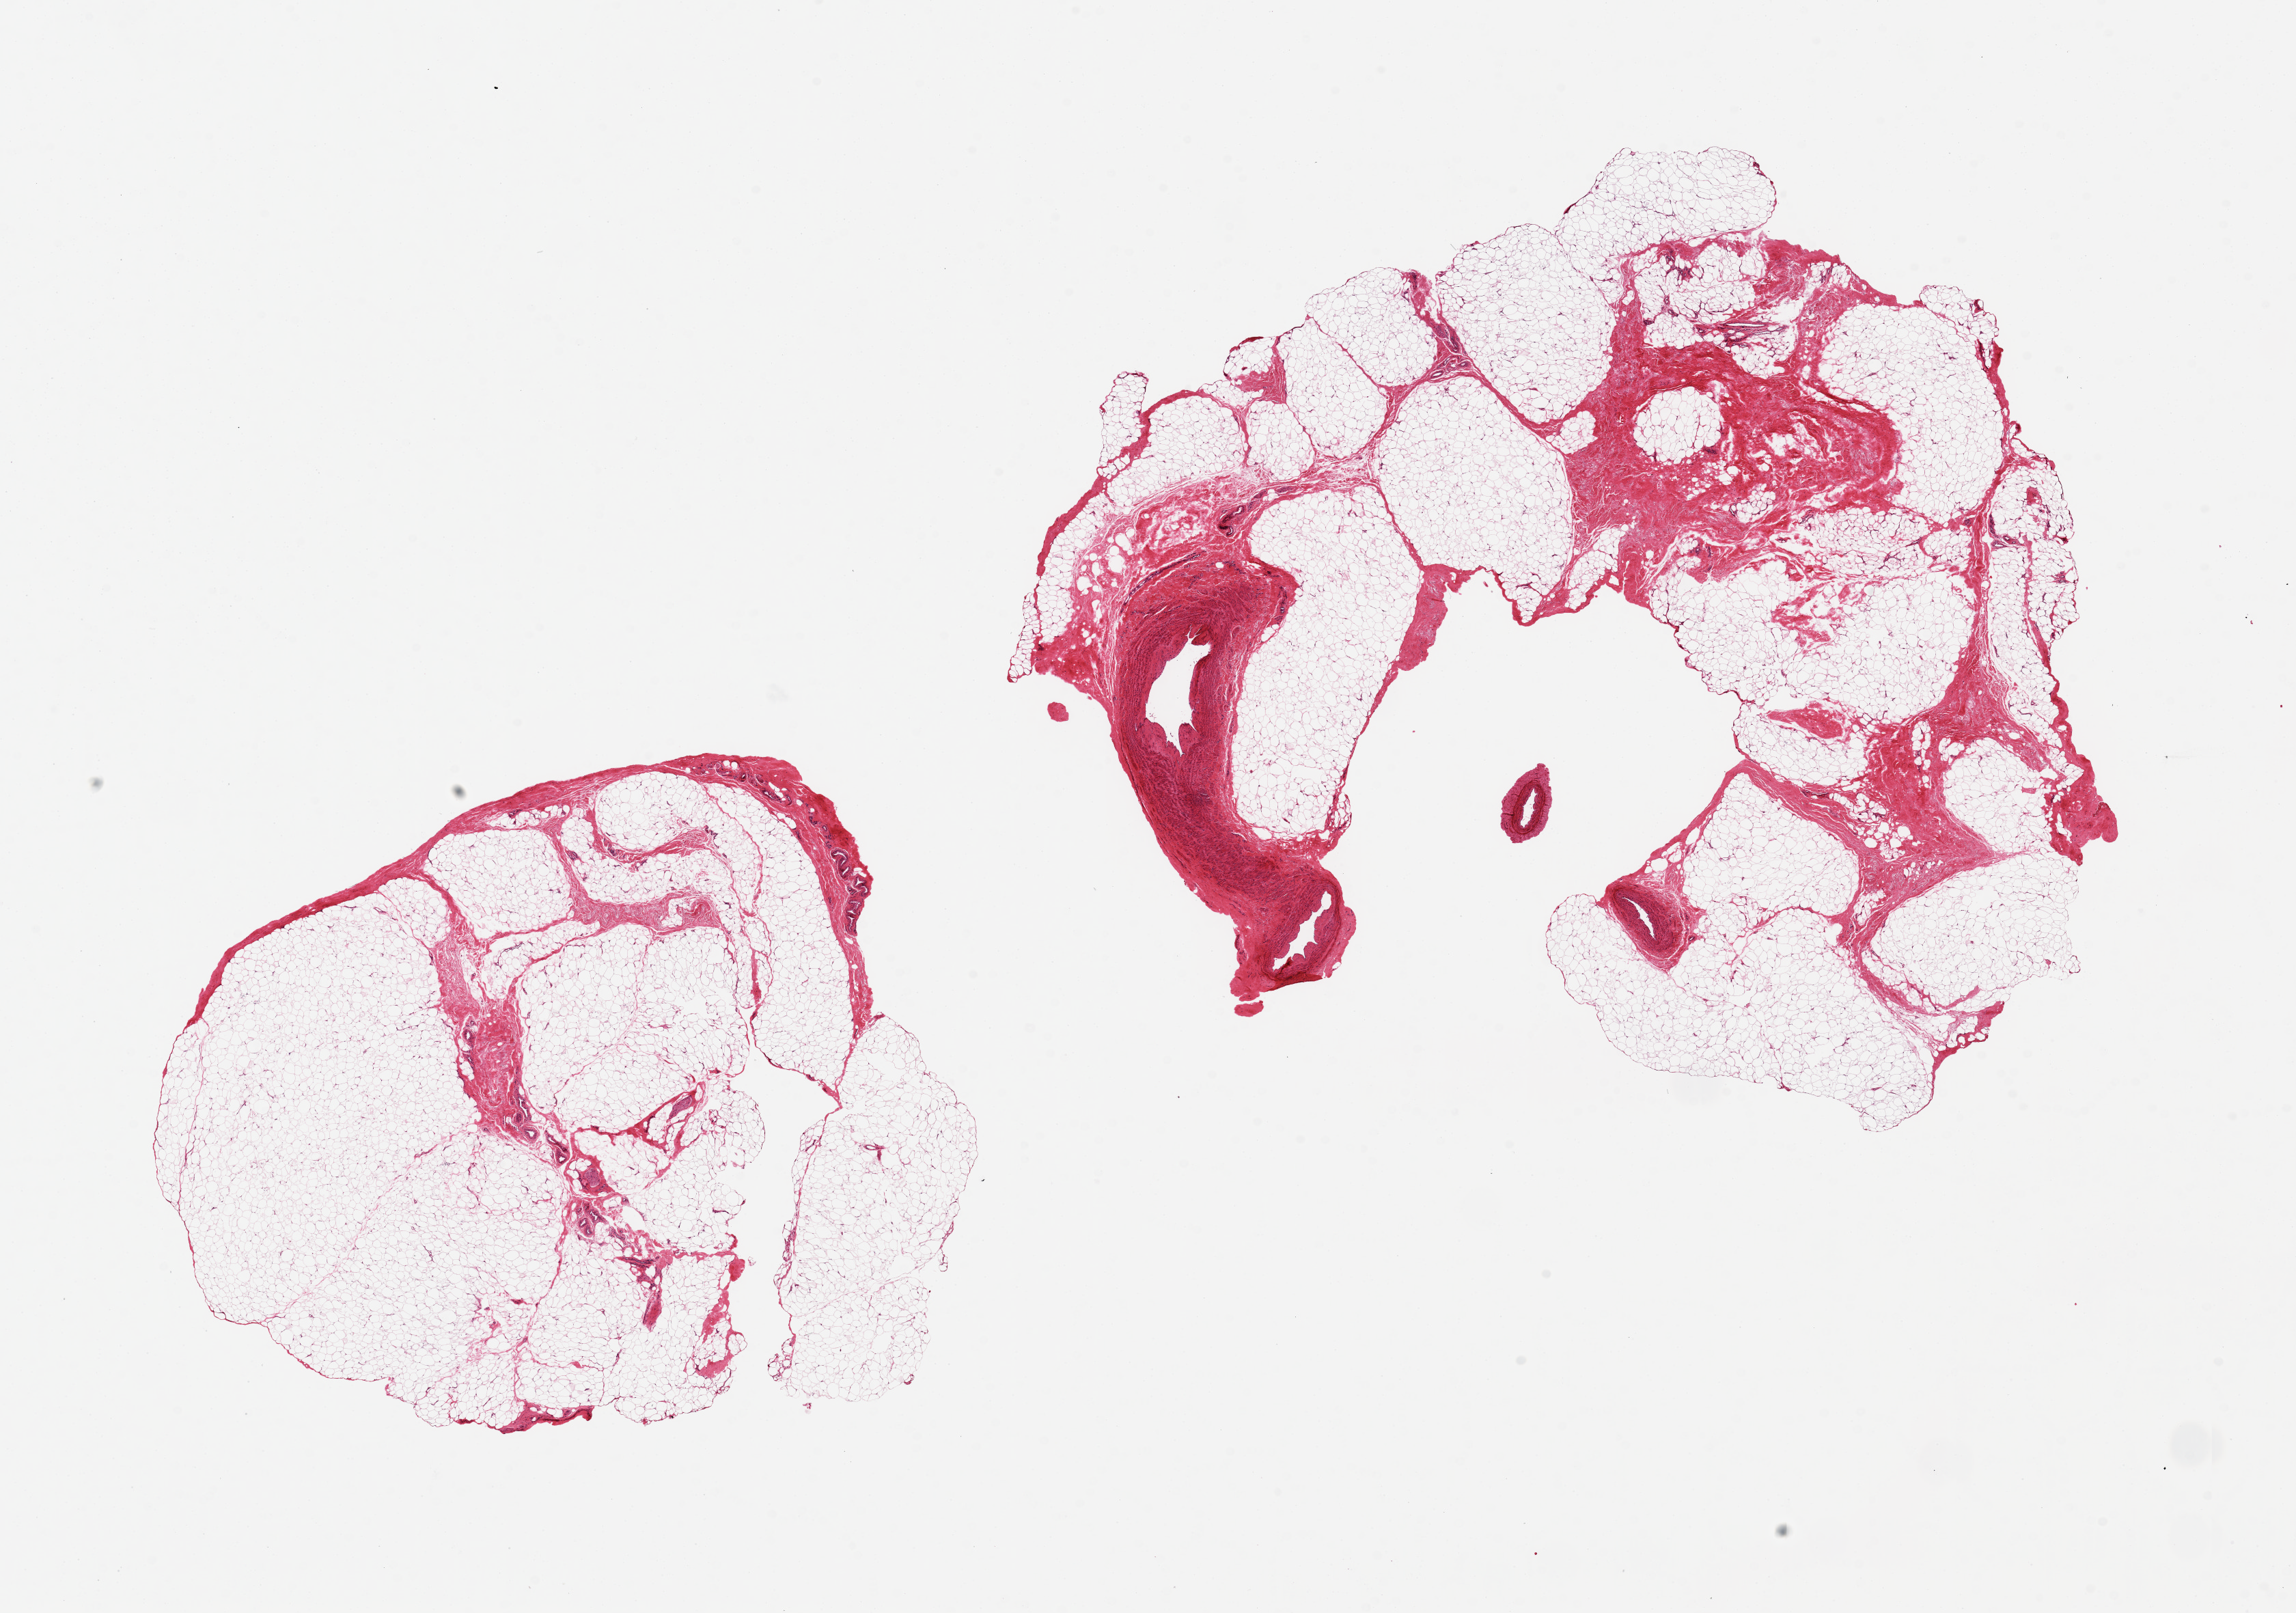
Digitized haematoxylin and eosin-stained section, brightfield, whole scanned area (about 26.6 x 18.7 mm, from a 20x scan) shown as a low-resolution overview, PAXgene-fixed, paraffin-embedded tissue, target tissue: adipose tissue, tissue donor sample. Male donor.
Reviewer comment on this tissue sample: 2 pieces, ~10x9mm.